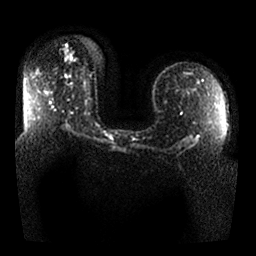
Breast MRI, one axial slice; slice 14 of 25 in the series (ordered by position); diffusion-weighted series; image 2 of 4 stored at this slice position (different b-values; order by instance number); 1.5 T; 256 × 256 image matrix, field of view 360 × 360 mm. Female patient.
Annotated regions visible in this slice (outlined manually by an expert reader):
- tumour on diffusion-weighted imaging: bounding box <65,51,74,61> (left, top, right, bottom; pixels)